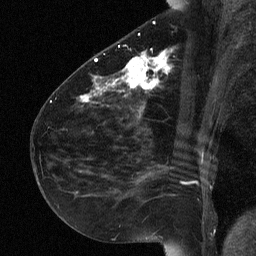
Breast MRI (dynamic contrast-enhanced), one sagittal slice. Position 32 of 64 along the scan axis. Dynamic contrast-enhanced study with each time point stored as its own series, time point 2 of 3 at this slice position (early post-contrast, ordered by acquisition time). 1.5 T. TE 4.8 ms, TR 27 ms. 2 mm slice thickness. 256 × 256 image matrix. Female patient, age 51 years. Case-level facts recorded for this patient, not image findings: setting: breast cancer imaged before/during neoadjuvant chemotherapy; receptor status: HR-positive, HER2-negative.
Annotated regions visible in this slice (semi-automatic segmentation, software-assisted and operator-edited):
- analysis volume of interest (the breast-tissue region the enhancement analysis was run in; not a lesion): bounding box <72,34,182,118> (left, top, right, bottom; pixels)
- tumour enhancement mask (voxels above the 90 % enhancement threshold inside the analysis volume of interest): <80,53,169,102>